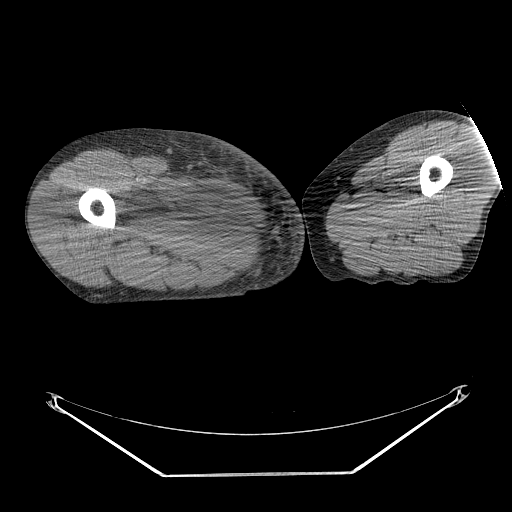
CT of an extremity soft-tissue mass (from a PET/CT study), one axial slice. Position 242 of 311 along the scan axis. Soft-tissue window (W 400 / L 40 HU). 3.75 mm slice thickness. 512 × 512 image matrix, field of view 500 × 500 mm. Male patient. Case-level facts recorded for this patient, not image findings: histological type: undifferentiated - pleiomorphic; grade: high; site of the primary tumour: right thigh.
Outlined on this slice (expert contour drawn on MRI and transferred to this co-registered scan by the dataset authors):
- gross tumour volume including surrounding oedema: box from (x=130, y=176) to (x=220, y=241) px
- gross tumour volume (mass): (x=167, y=187)–(x=220, y=232)